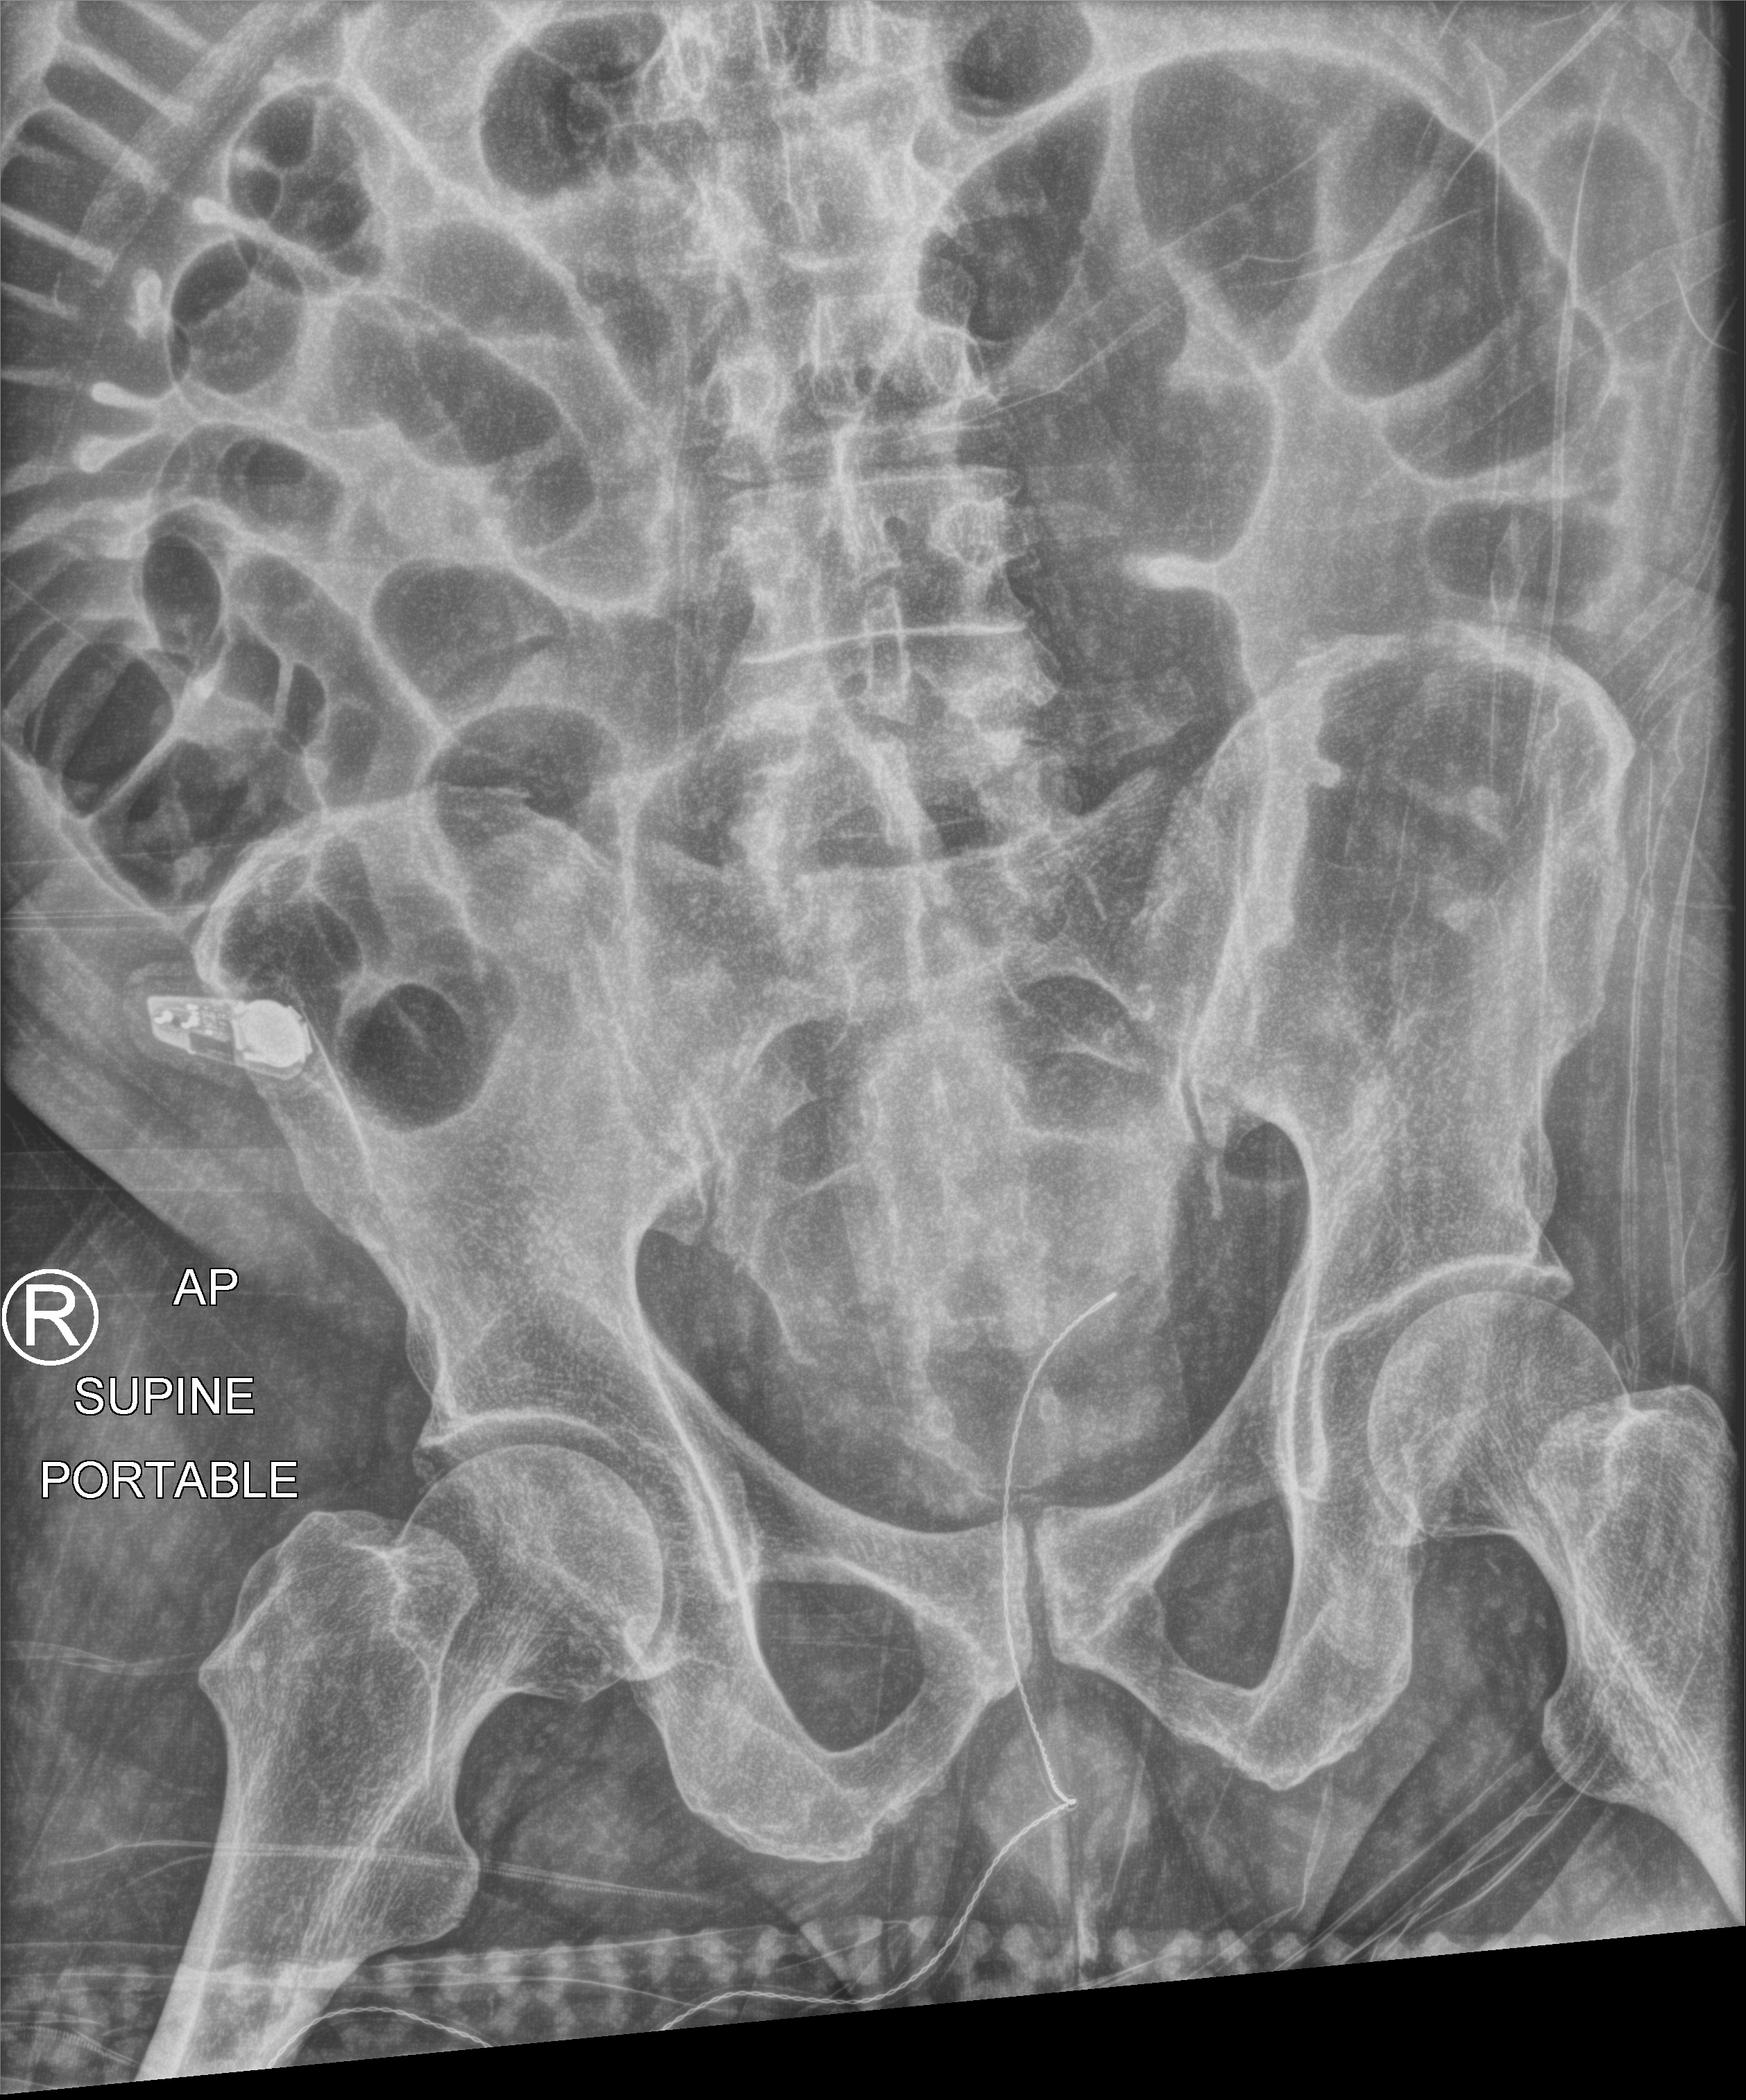
Bedside abdomen radiograph (computed radiography); anteroposterior (AP) projection. Patient hospitalised with COVID-19; male, aged 18–59 years.
From the hospital-stay record, not from the radiograph (when in the stay this image was taken is not recorded): other chronic lung disease (admission record): yes; COPD (admission record): yes; length of hospital stay: 63 days.